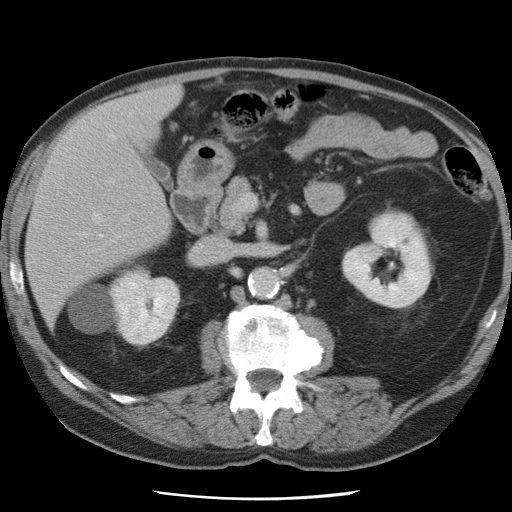
Contrast-enhanced abdominal CT, one axial slice. Position 35 of 78 along the scan axis. Intravenous contrast given. Soft-tissue window (W 400 / L 40 HU). 5 mm slice thickness. 512 × 512 image matrix. Male patient, age 75 years. From the clinical record (not read from this slice): diagnosis: colorectal cancer liver metastases, imaged before liver resection.
Annotated regions visible in this slice (manually delineated by an expert):
- hepatic veins: bounding box (x1, y1, x2, y2) in pixels: (78, 134, 115, 238)
- liver: (26, 86, 181, 320)
- planned liver remnant (the part of the liver to remain after resection): (26, 117, 171, 321)
- portal vein (with intrahepatic branches): (108, 179, 112, 183)